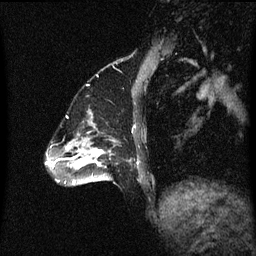
Breast MRI (dynamic contrast-enhanced), one sagittal slice; slice 17 of 60 in the series (ordered by position); dynamic contrast-enhanced series, image 2 of 3 at this slice position (ordered by acquisition); 1.5 T; TE 4.2 ms, TR 8.4 ms; 2 mm slice thickness; 256 × 256 image matrix. Patient: female, 47 years.
Outlined on this slice (semi-automatic segmentation, software-assisted and operator-edited):
- analysis volume of interest (the breast-tissue region the enhancement analysis was run in; not a lesion): bounding box <85,138,117,185> (left, top, right, bottom; pixels)
- tumour enhancement mask (voxels above the 70 % enhancement threshold inside the analysis volume of interest): <92,150,105,181>